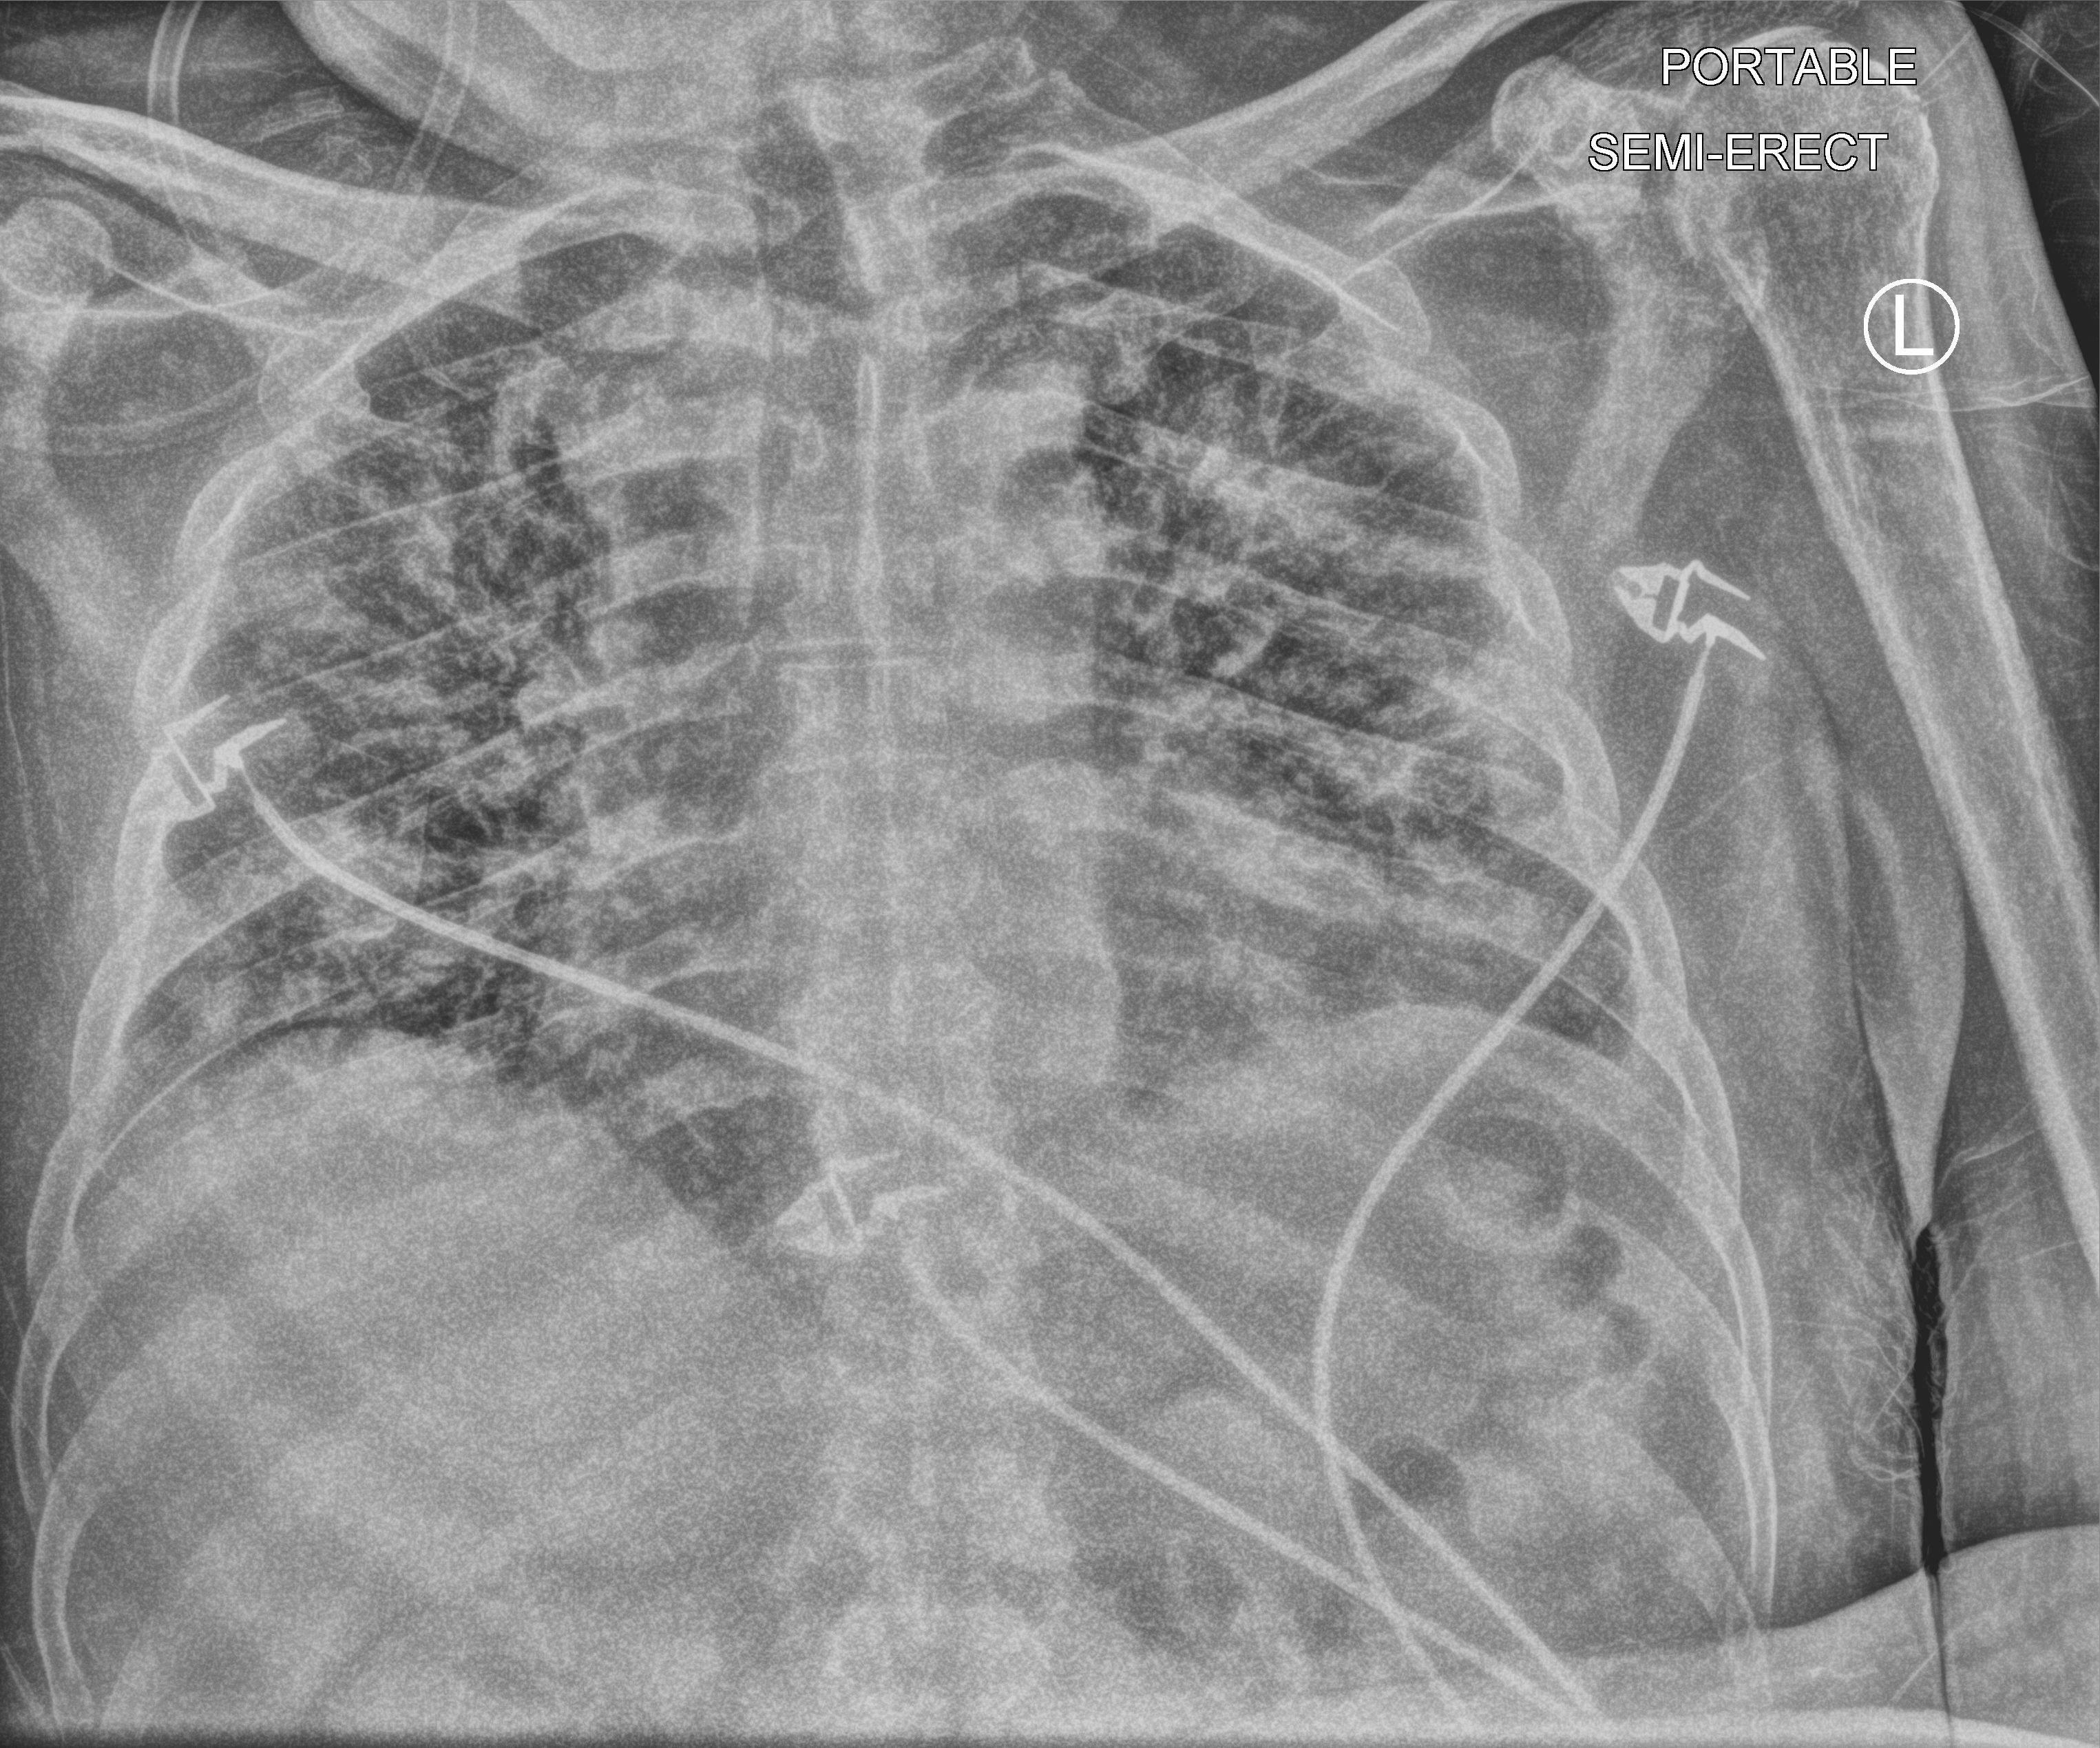
Portable chest radiograph, anteroposterior (AP) projection. Patient hospitalised with COVID-19; male, aged 60–74 years.
Admission-level facts for this patient (not findings on this image; timing relative to this image not recorded):
- diabetes (admission record): yes